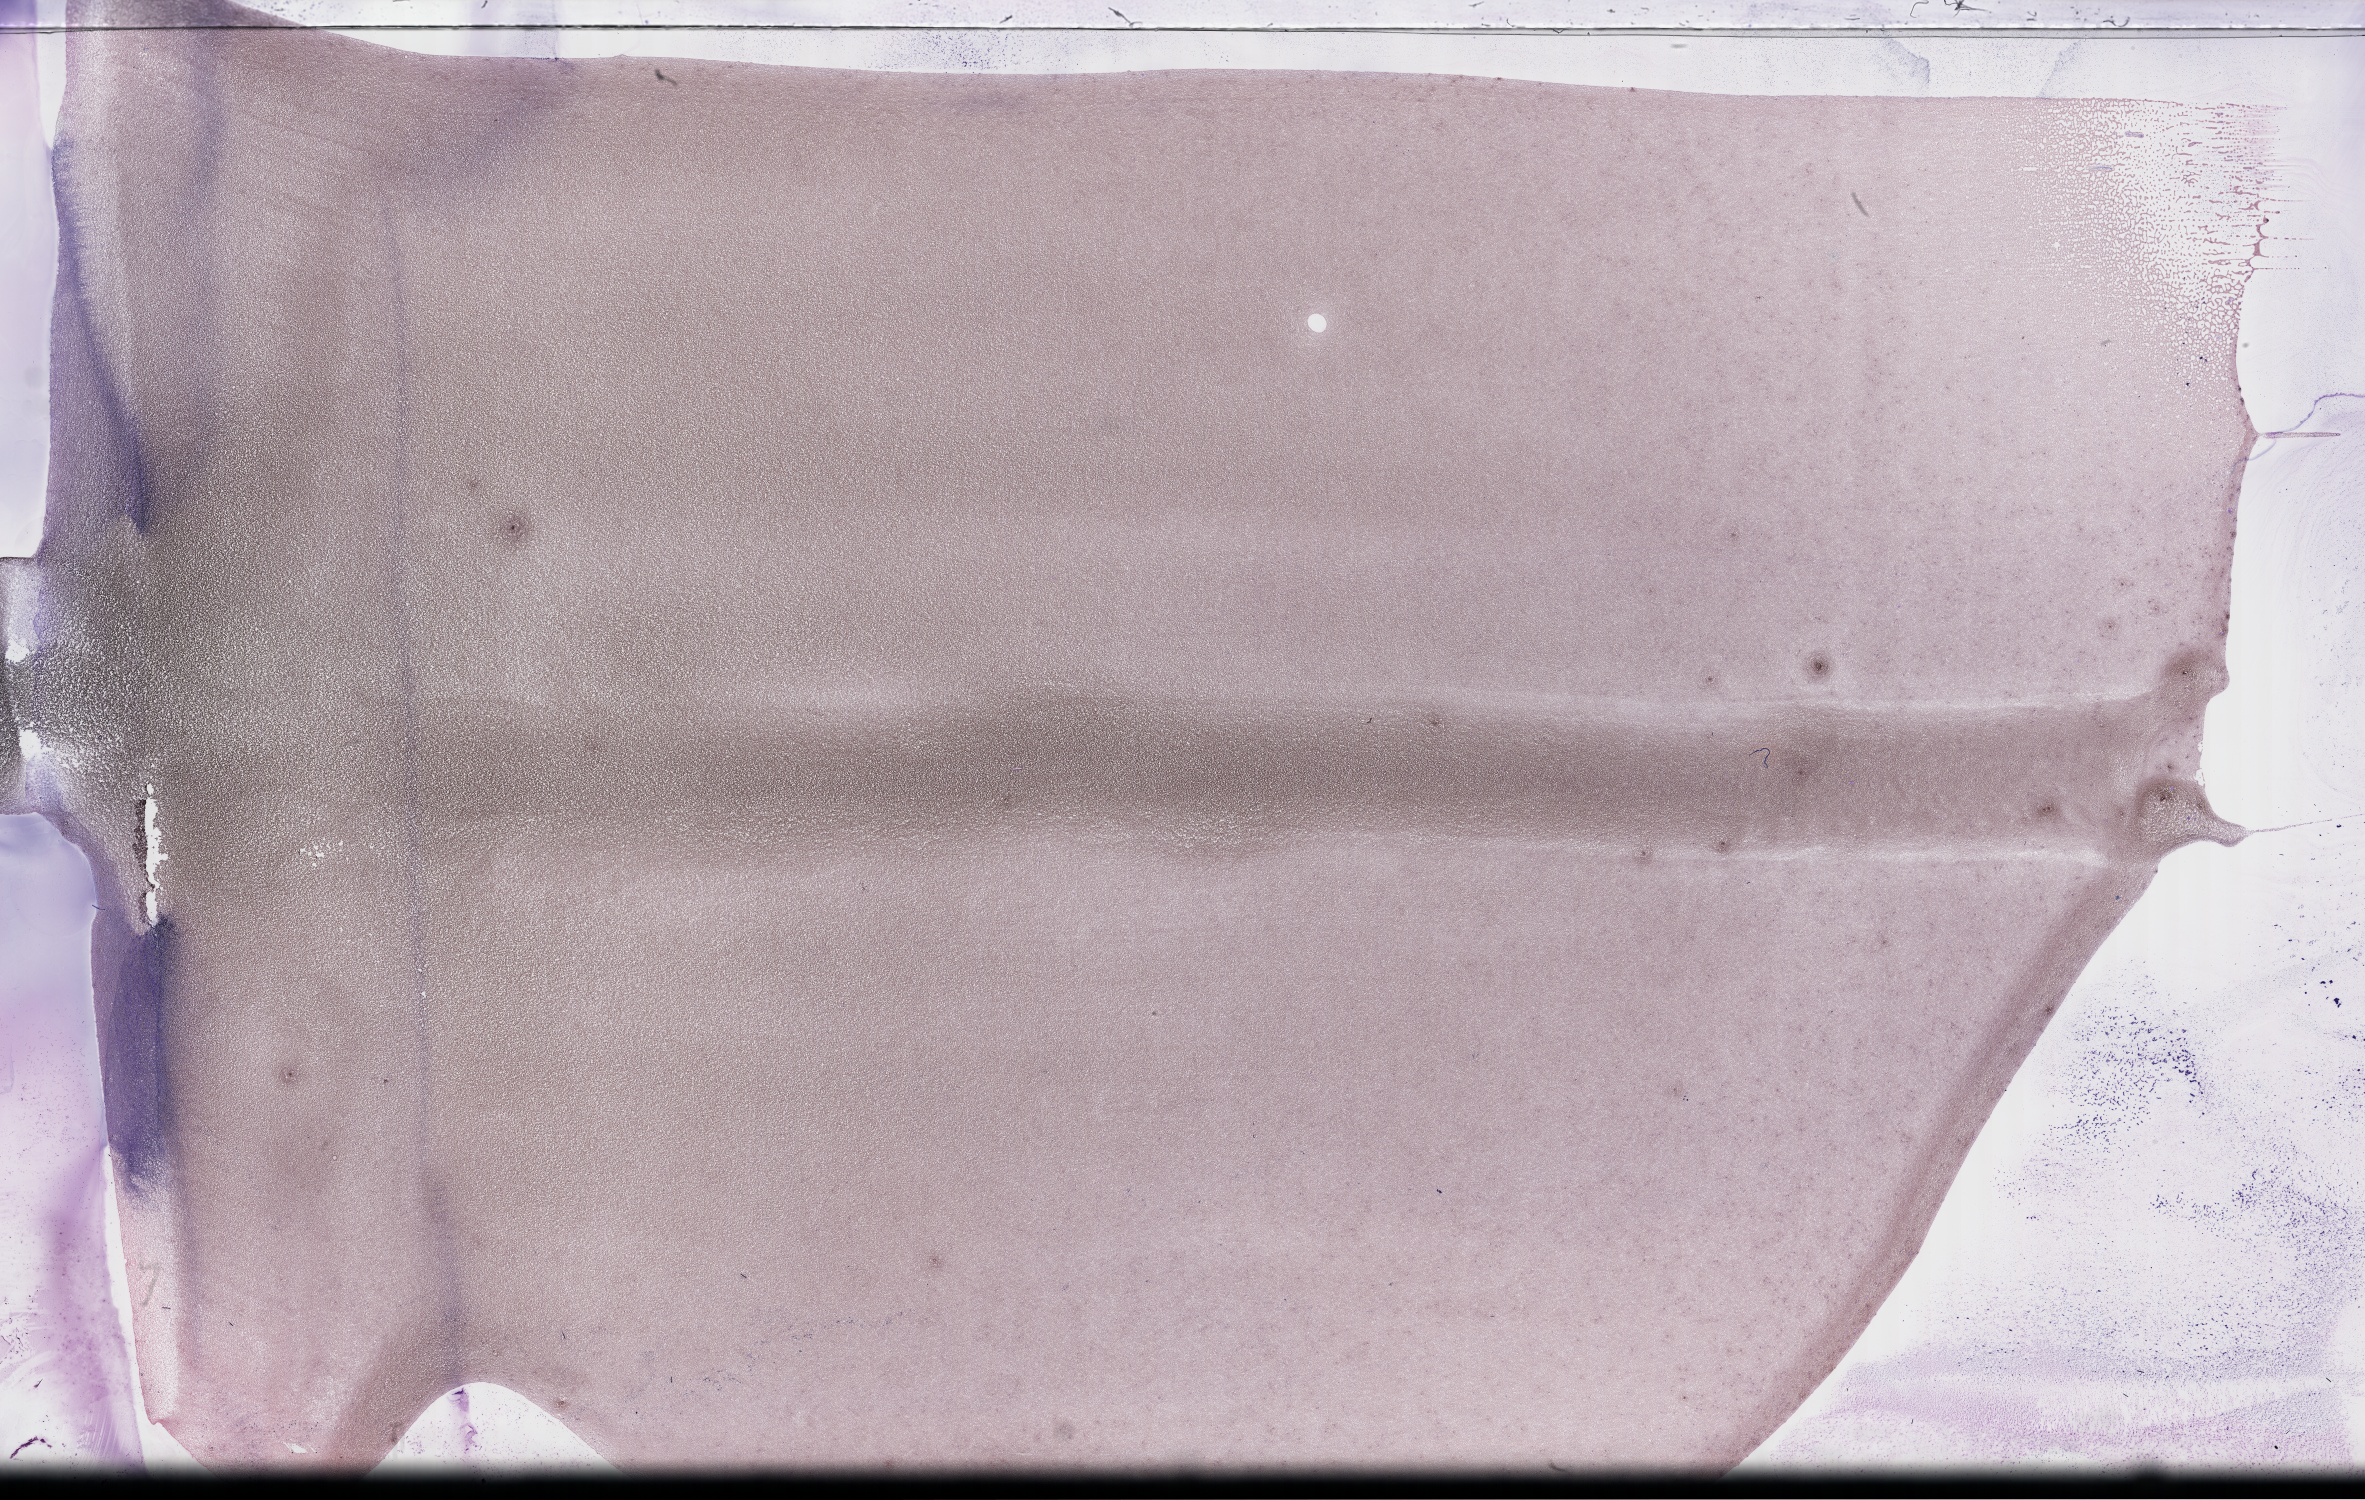
Wright–Giemsa-stained whole blood smear, whole-slide image — low-resolution overview of the scanned area, about 38.2 x 24.2 mm. Patient sex: male.
From a patient with: Plasma Cell Myeloma.